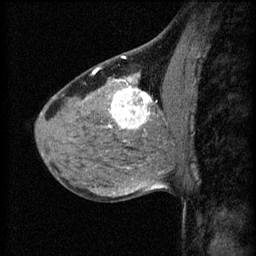
Breast MRI (dynamic contrast-enhanced), one sagittal slice; slice 30 of 60 in the series (ordered by position); 3 images stored at this slice position (order not interpretable as contrast timing); 1.5 T; TE 4.2 ms, TR 8.2 ms; 2.2 mm slice thickness; 256 × 256 image matrix, field of view 180 × 180 mm. Patient: female, 40 years.
Outlined on this slice (semi-automatically segmented with operator editing):
- analysis volume of interest (the breast-tissue region the enhancement analysis was run in; not a lesion): box from (x=108, y=82) to (x=175, y=139) px
- tumour enhancement mask (voxels above the 70 % enhancement threshold inside the analysis volume of interest): (x=108, y=82)–(x=153, y=129)